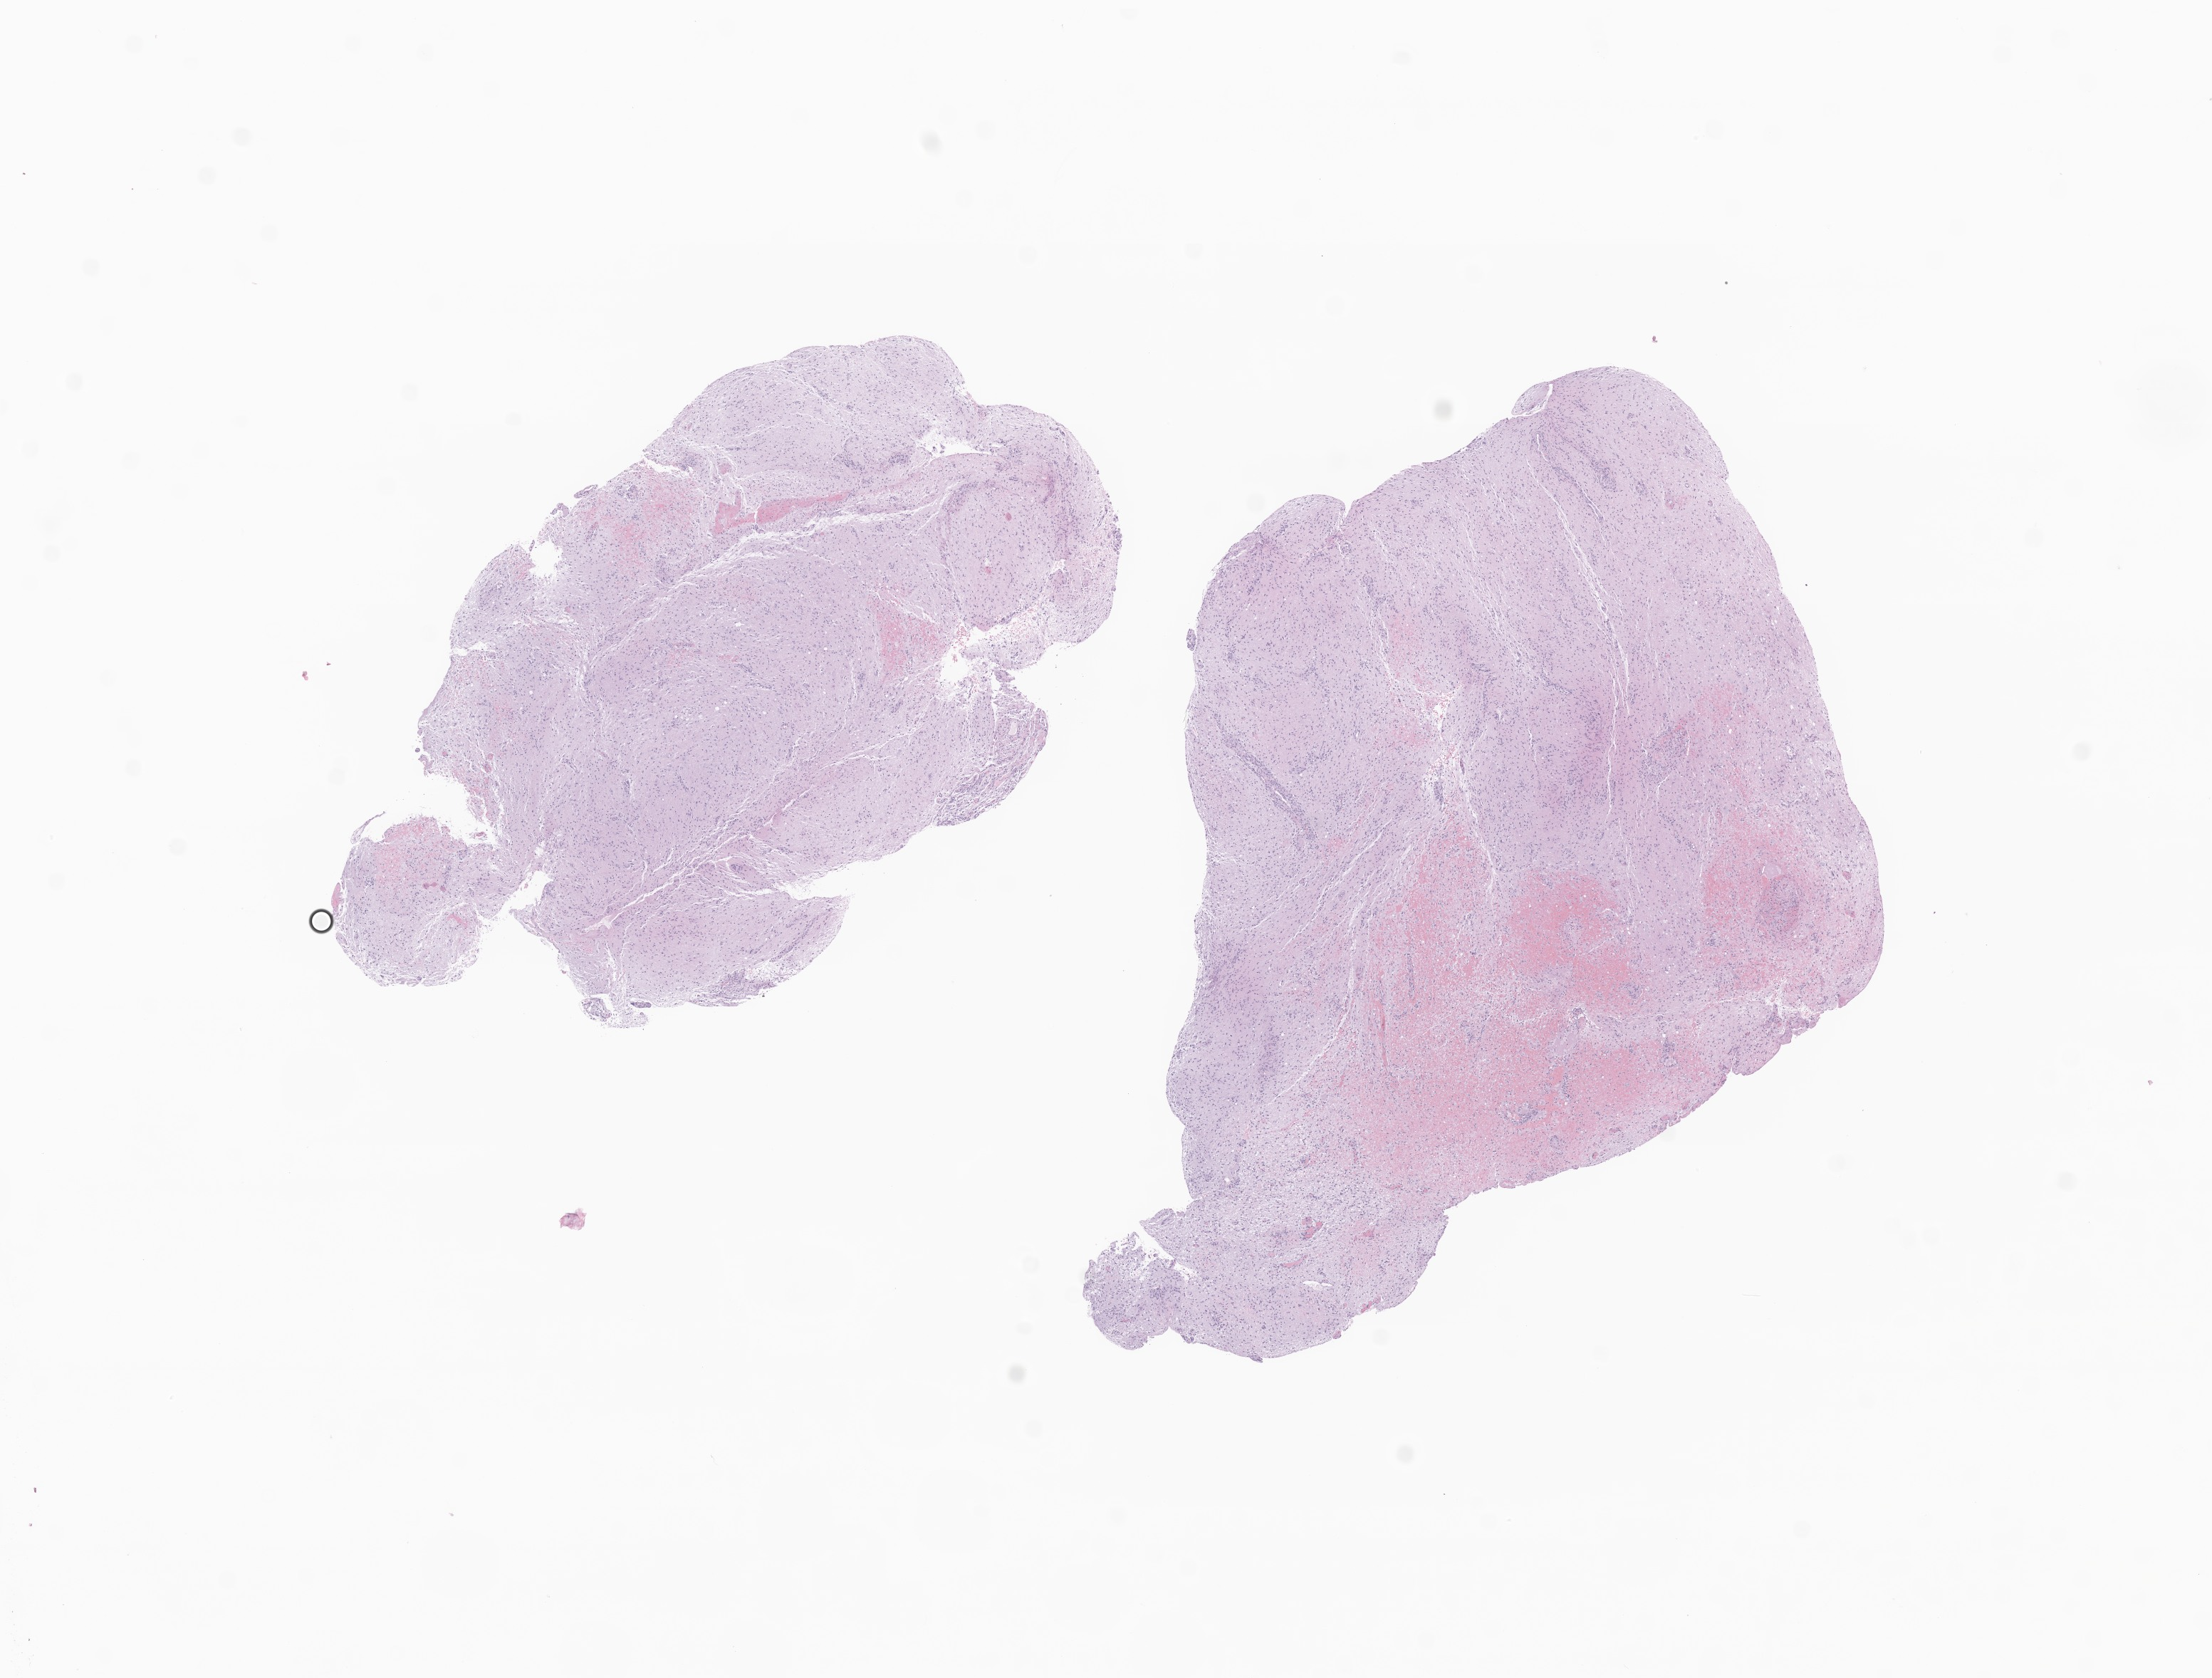
Hematoxylin and eosin (H&E) whole-slide image of tumor tissue from the central nervous system, shown as a low-resolution overview of the whole scanned area (about 13.1 x 9.9 mm); formalin-fixed paraffin-embedded section. Female patient, age 35 months (2 years 11 months).
* diagnosis: Glioma, malignant